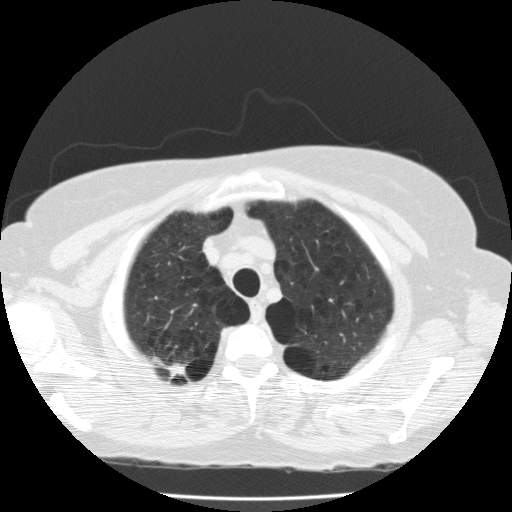
Chest CT (low-dose screening protocol), one axial image. Second annual screen. Lung window (W 1500 / L -600 HU). 120 kVp. Slice 25 of 174 in the series. Female participant, aged 59 years at enrolment. Current smoker at enrolment.
Lesion marked by an expert reader, bounding box <141,347,196,392> (left, top, right, bottom; pixels). Reader record for this screening exam (exam-level; its link to the box is not recorded): non-calcified nodule or mass ≥4 mm, right upper lobe, 11 × 6 mm, spiculated (stellate) margins, soft tissue attenuation, pre-existing on the prior screen: yes; interval growth: no. Official screen result: positive, no significant change: stable abnormalities potentially related to lung cancer, unchanged since the prior screening exam. Later outcome: lung cancer diagnosed 490 days after this screen — adenocarcinoma, NOS, right upper lobe, poorly differentiated (G3), stage IA (AJCC 6th edition), 20 mm at pathology.